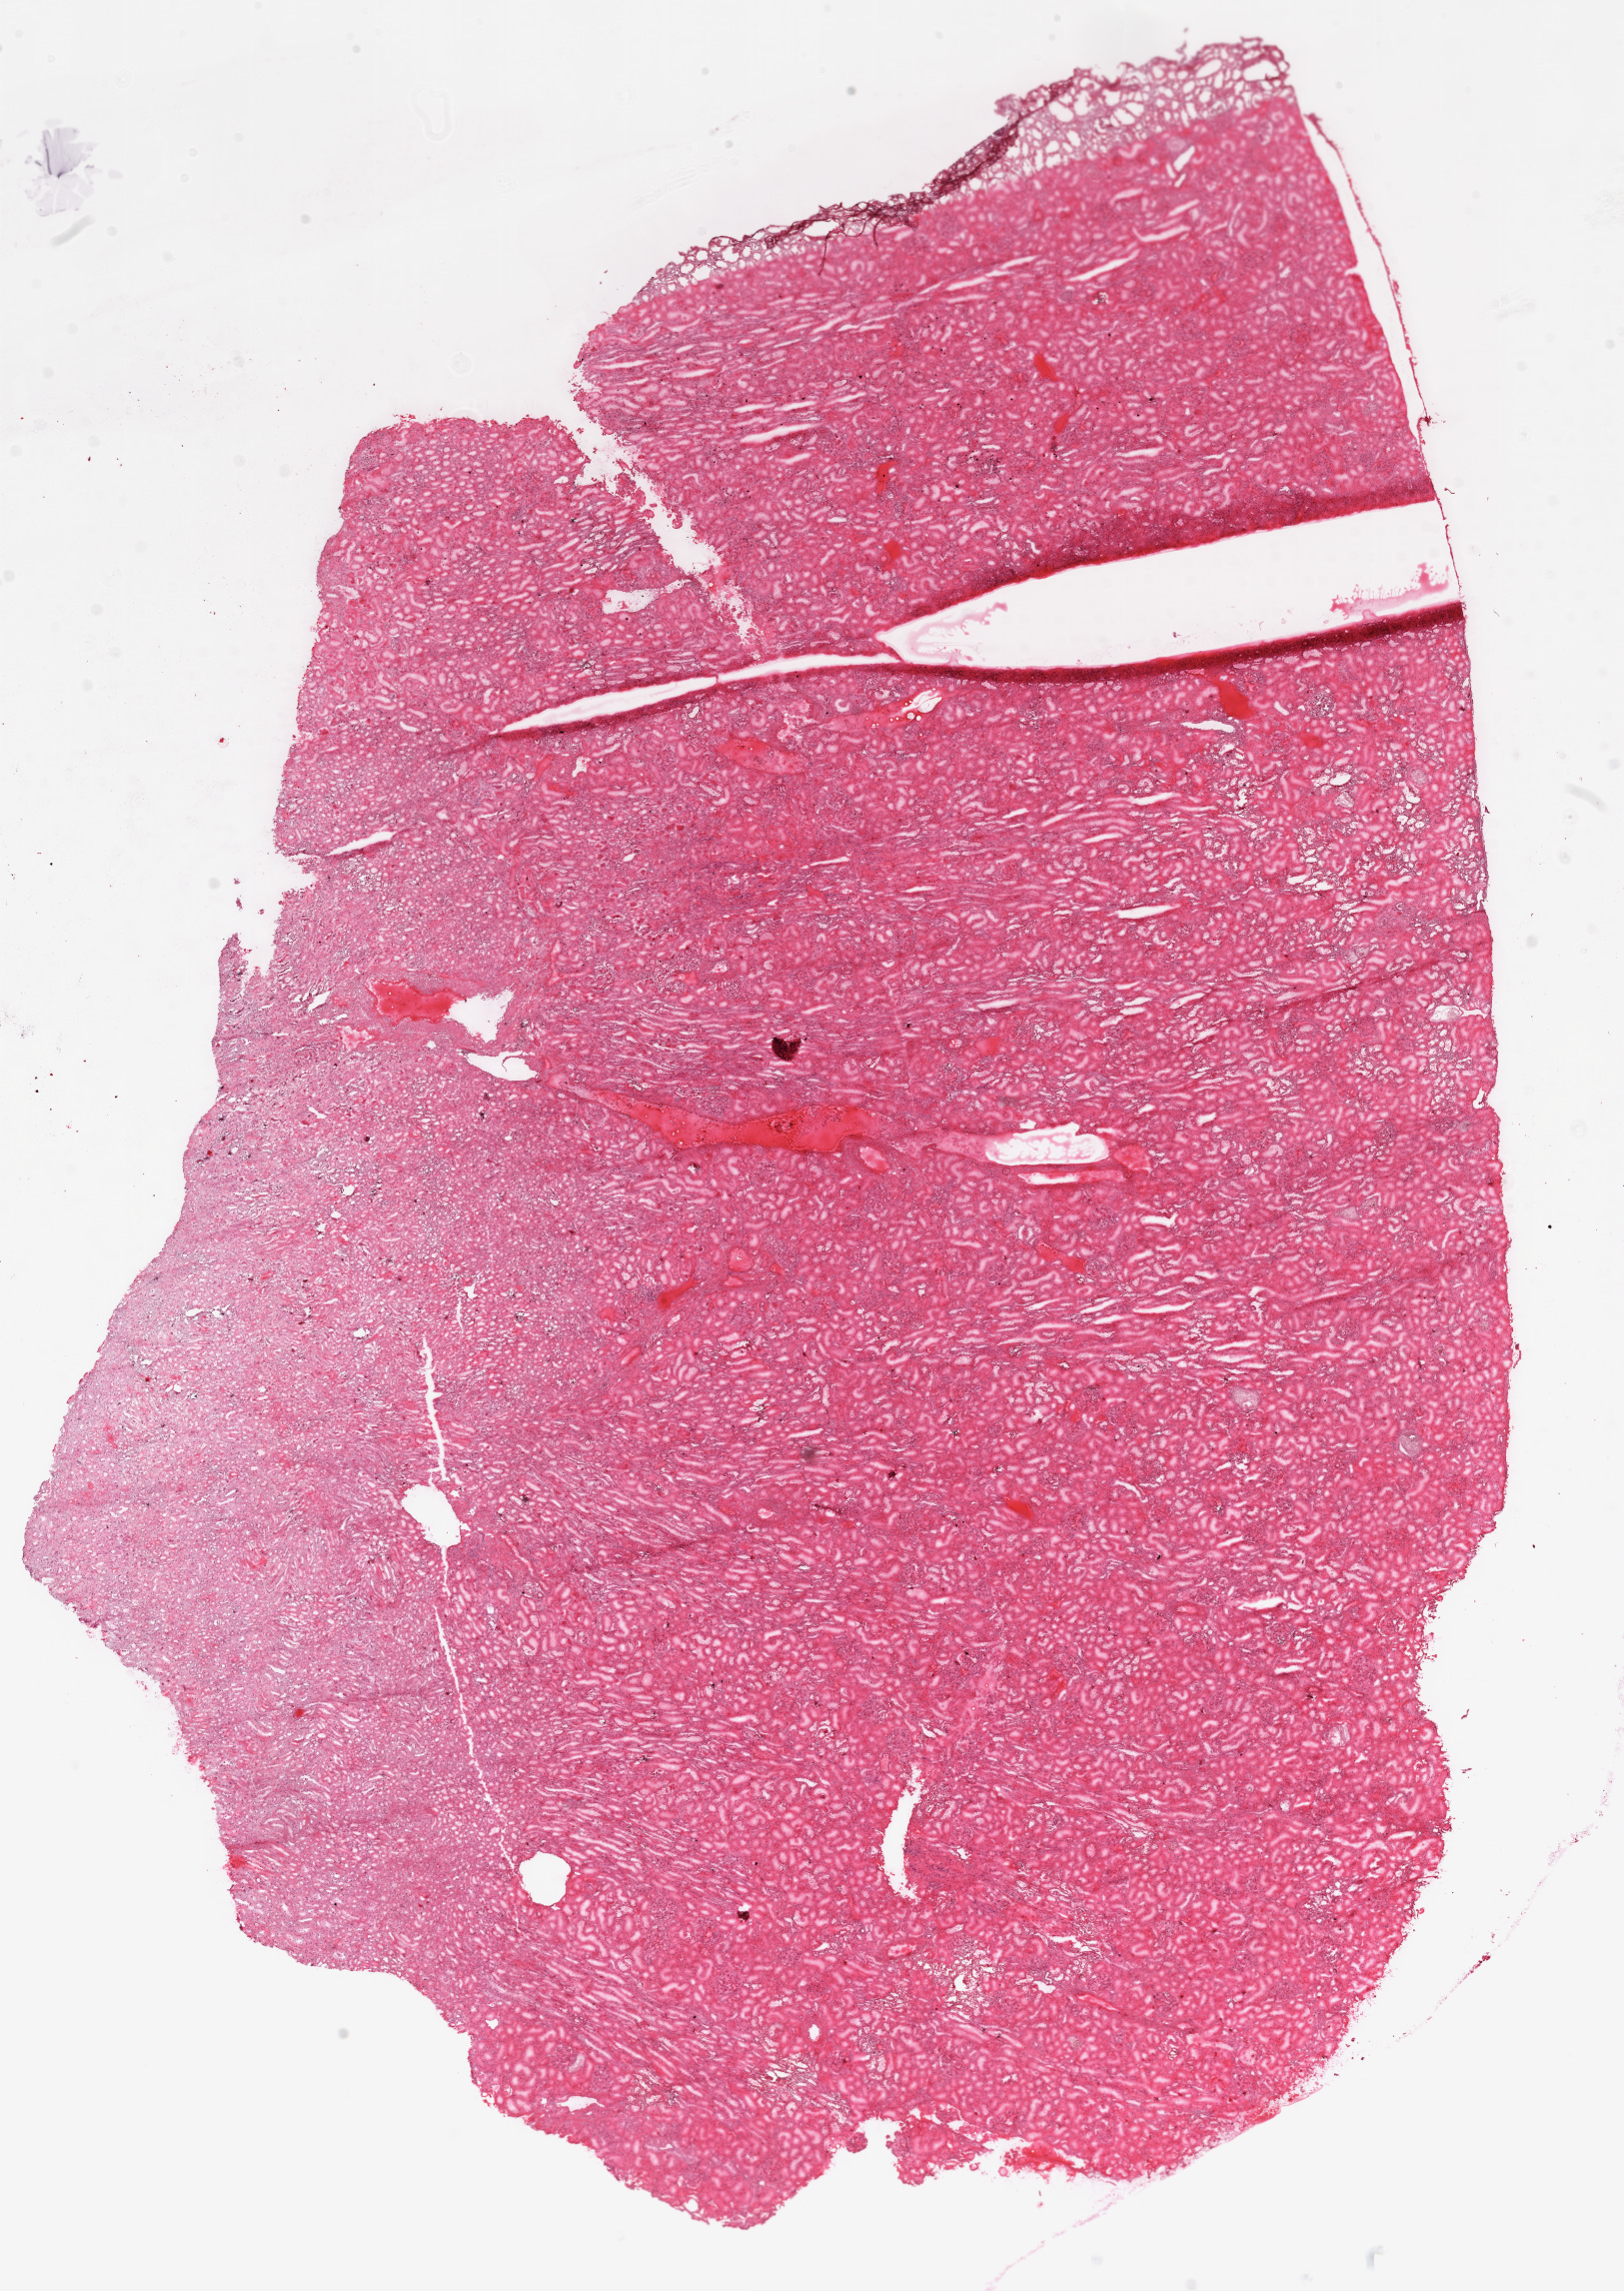
Hematoxylin and eosin (H&E) stained whole-slide image, whole scanned area (about 13.0 x 18.4 mm) shown as a low-resolution overview. Frozen section. Solid tissue normal (non-tumour tissue) sample from the kidney. Male patient; age at initial diagnosis 59 years.
This section: solid tissue normal sample (biorepository sample class). Patient diagnosis: Clear cell adenocarcinoma, NOS.